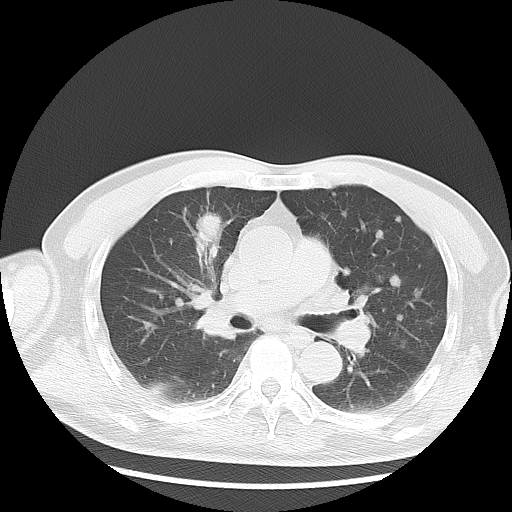
Chest CT, one axial slice. 120 kVp. Lung window (W 1500 / L -600 HU). 5 mm slice thickness. 512 × 512 image matrix, field of view 369 × 369 mm. Patient: male, 57 years. From the clinical record (not read from this slice): clinical TNM (as recorded): T2 N3 M1a.
Structures marked on this image (rectangle marked by the reading radiologist):
- lung tumour (recorded histology: adenocarcinoma): bounding box <196,212,222,251> (left, top, right, bottom; pixels)